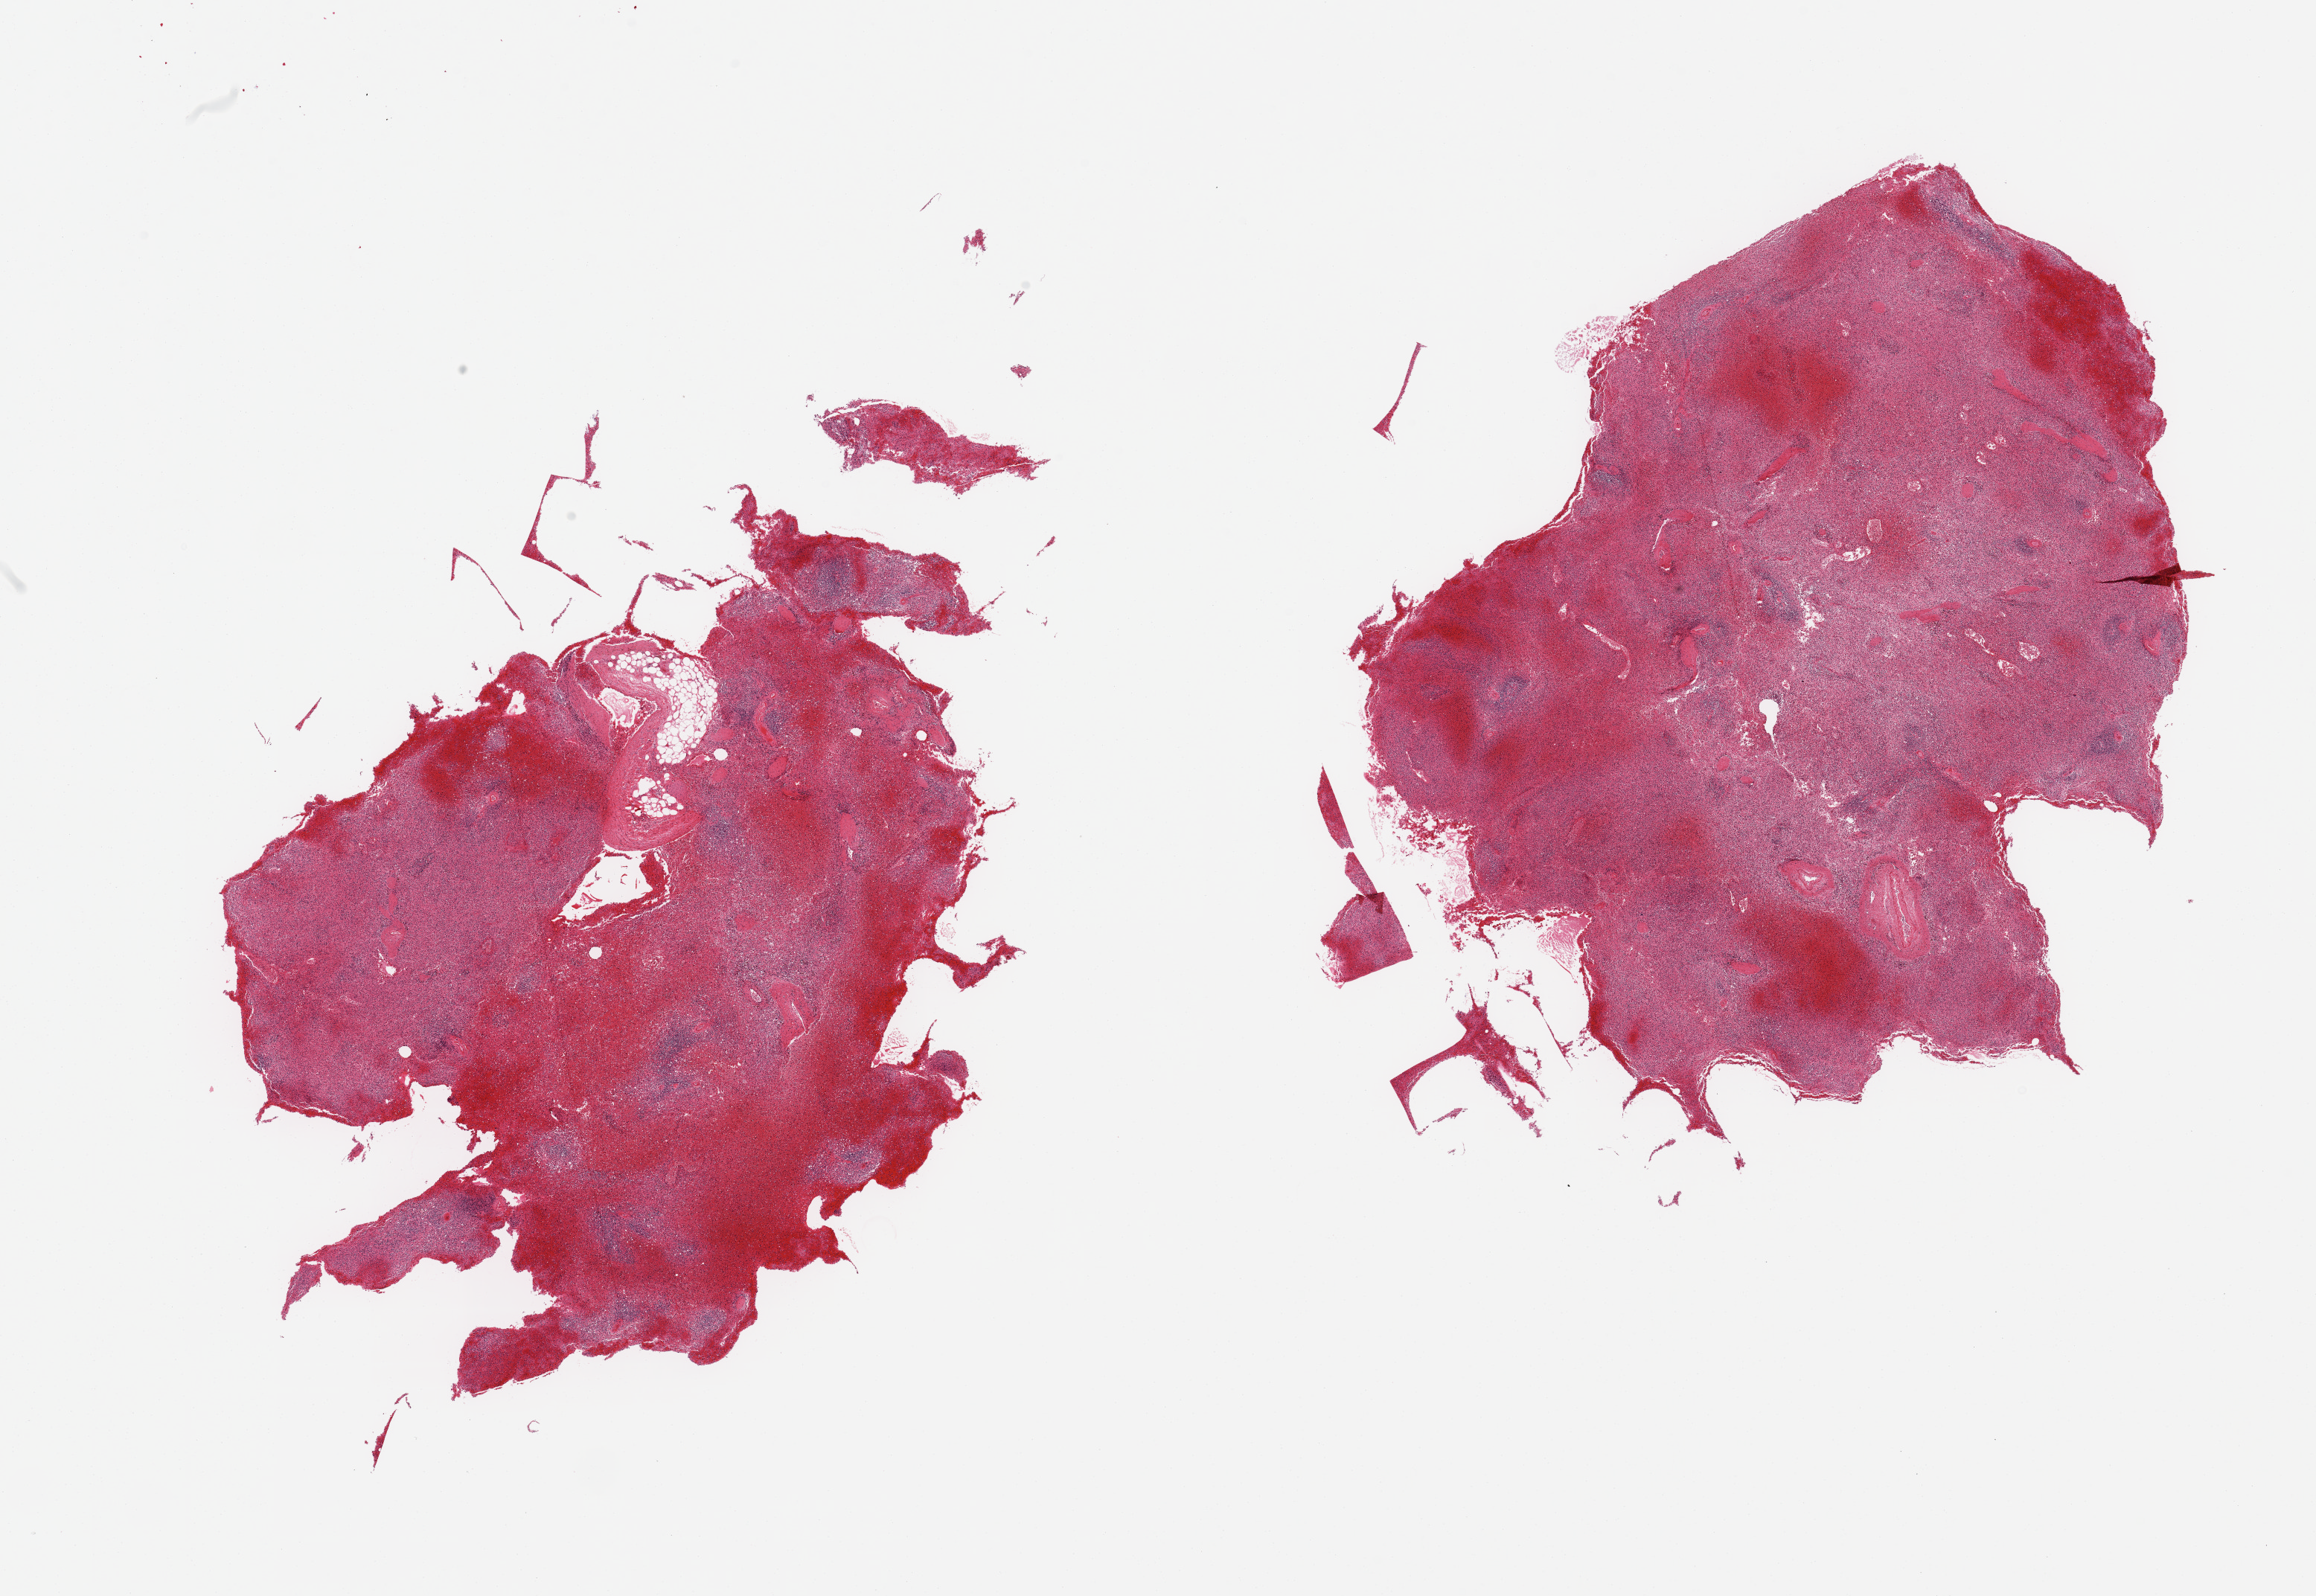
Hematoxylin and eosin (H&E) whole-slide image, shown as a low-resolution overview of the whole scanned area (about 24.6 x 17.0 mm); PAXgene-fixed, paraffin-embedded tissue; target tissue: spleen; tissue donor sample. Donor: male.
Review note (as recorded): 2 pieces; congestion.